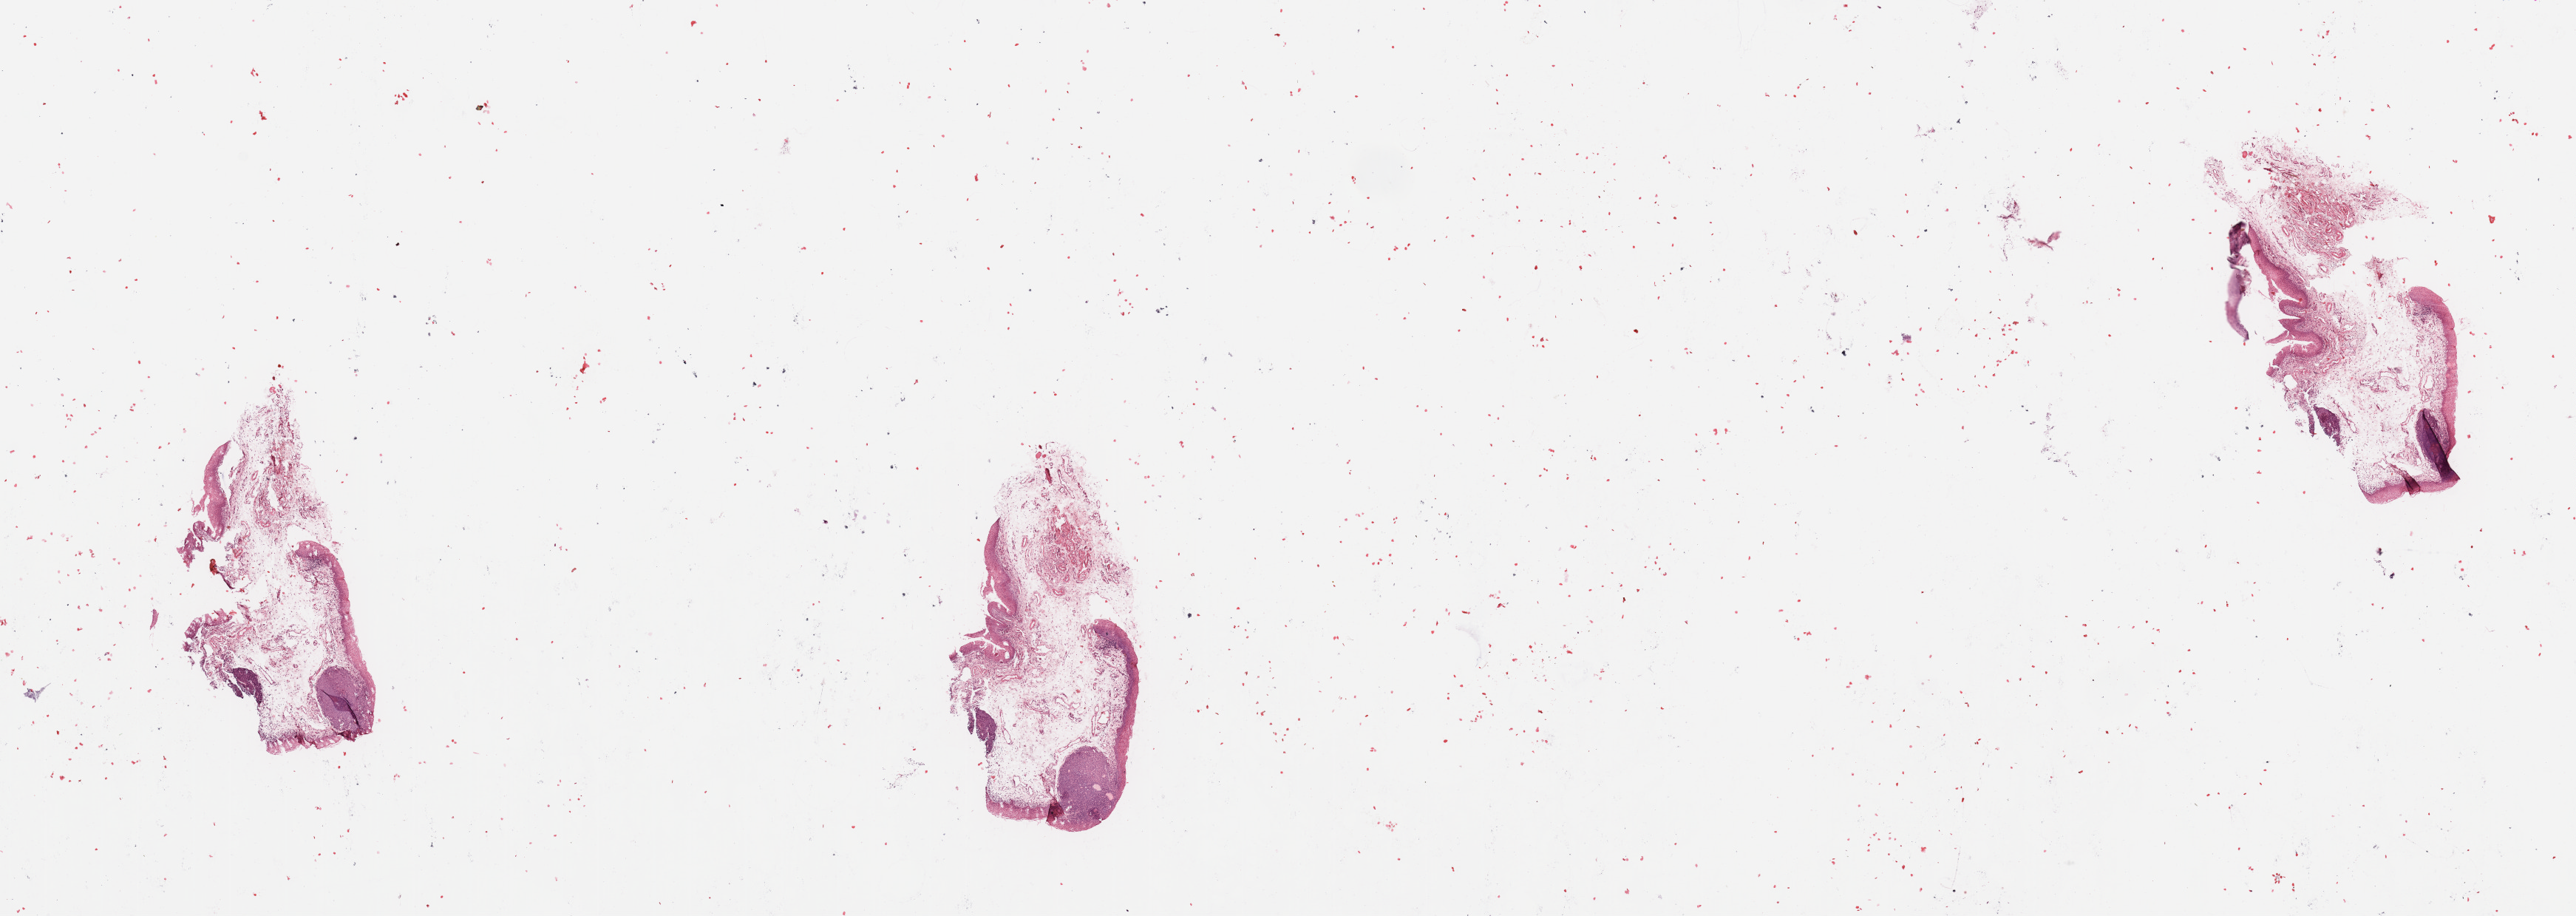
Whole-slide histology image, Hematoxylin and eosin (H&E) stained, low-resolution overview of the scanned area, about 27.6 x 9.8 mm. Head and neck, normal (non-tumour) tissue. Patient: male, age 62 years.
• this section: normal (non-tumour) tissue from the same patient
• patient diagnosis: Squamous cell carcinoma, NOS (larynx, NOS)